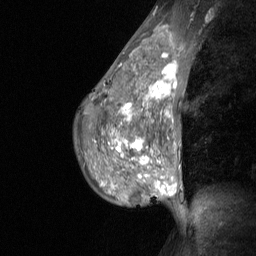
Breast MRI (dynamic contrast-enhanced), one sagittal slice. Position 42 of 64 along the scan axis. Dynamic contrast-enhanced study with each time point stored as its own series, time point 2 of 3 at this slice position (early post-contrast, ordered by acquisition time). 1.5 T. TE 4.8 ms, TR 27 ms. 256 × 256 image matrix, field of view 200 × 200 mm. Patient: female, 36 years. Case-level facts recorded for this patient, not image findings: setting: breast cancer imaged before/during neoadjuvant chemotherapy; receptor status: HR-positive, HER2-negative.
Outlined on this slice (semi-automatically segmented with operator editing):
- analysis volume of interest (the breast-tissue region the enhancement analysis was run in; not a lesion): bounding box <75,45,187,210> (left, top, right, bottom; pixels)
- tumour enhancement mask (voxels above the 90 % enhancement threshold inside the analysis volume of interest): <113,53,178,195>